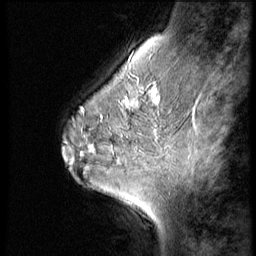
Breast MRI (dynamic contrast-enhanced), one sagittal slice; 3 images stored at this slice position (order not interpretable as contrast timing); 1.5 T; TE 4.2 ms, TR 9 ms; 256 × 256 image matrix. Patient: female, 45 years. From the clinical record (not read from this slice): setting: breast cancer imaged before/during neoadjuvant chemotherapy; receptor status: HR-positive, HER2-negative.
Outlined on this slice (semi-automatically segmented with operator editing):
- analysis volume of interest (the breast-tissue region the enhancement analysis was run in; not a lesion): bounding box (x1, y1, x2, y2) in pixels: (102, 77, 166, 129)
- tumour enhancement mask (voxels above the 140 % enhancement threshold inside the analysis volume of interest): (121, 84, 160, 129)